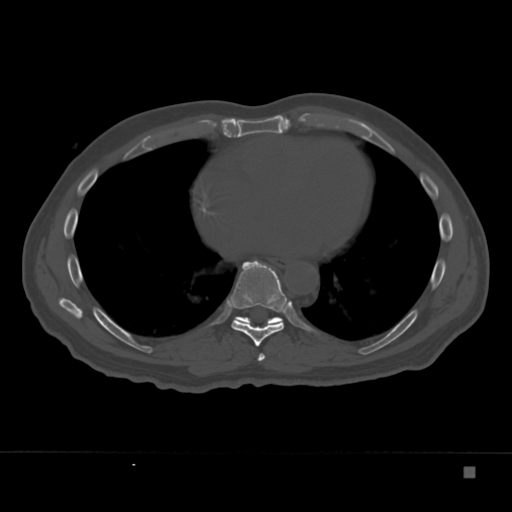
CT including the spine, one axial slice. Position 203 of 332 along the scan axis. Reconstruction kernel Br40s. 120 kVp. Bone window (W 1800 / L 400 HU). 1.5 mm slice thickness. 512 × 512 image matrix, field of view 389 × 389 mm. Male patient, age 72 years. Case-level facts recorded for this patient, not image findings: primary cancer: skeletal.
Structures marked on this image (semi-automatically segmented with operator editing):
- T7 vertebra: bounding box (x1, y1, x2, y2) in pixels: (258, 353, 265, 361)
- T8 vertebra: (227, 260, 289, 347)
- T9 vertebra: (234, 316, 284, 328)